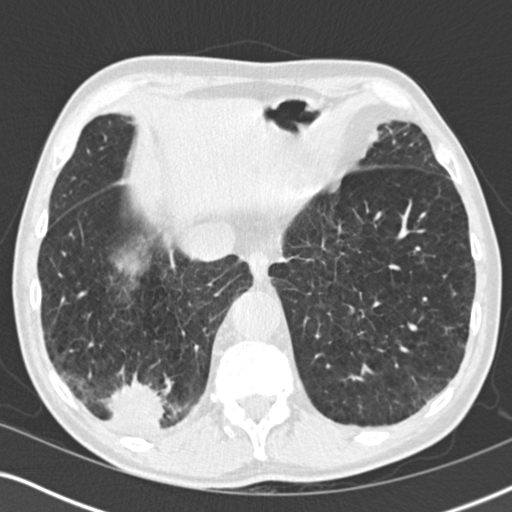
Low-dose screening chest CT, axial slice. Baseline screening round. Lung window (W 1500 / L -600 HU). 2 mm slice thickness. Standard (soft-tissue) reconstruction kernel (B30f). 120 kVp. Slice 143 of 196 in the series. Male participant, aged 64 years at enrolment. Former smoker at enrolment.
Expert reader's lesion annotation, bounding box (x1, y1, x2, y2) in pixels: (78, 365, 179, 451). The screening reader recorded 3 non-calcified nodules or masses ≥4 mm on this exam (lingula, lingula, right lower lobe); which of them this box marks is not recorded. Official screen result: positive, change unspecified: nodule(s) >= 4 mm or enlarging nodule(s), mass(es), or other non-specific abnormalities suspicious for lung cancer. Lung cancer was diagnosed 27 days after this screen: squamous cell carcinoma, NOS, right lower lobe, moderately differentiated (G2), stage IV (AJCC 6th edition), 40 mm at pathology.